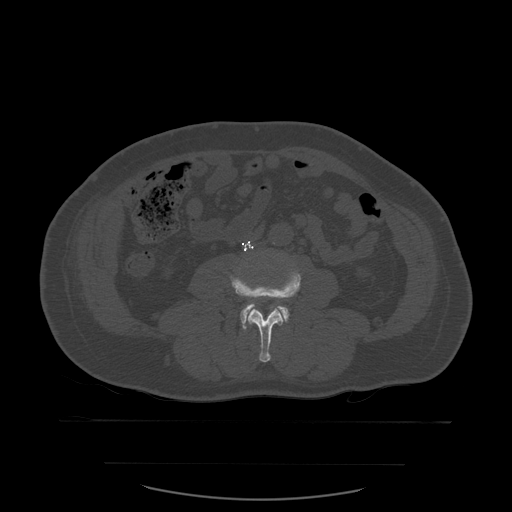
CT including the spine, one axial slice; position 183 of 590 along the scan axis; bone window (W 1800 / L 400 HU); 1.25 mm slice thickness; 512 × 512 image matrix, field of view 479 × 479 mm. Patient age 71 years. Case-level facts recorded for this patient, not image findings: primary cancer: lung.
Annotated regions visible in this slice (semi-automatically segmented with operator editing):
- L3 vertebra: bounding box <230,260,302,363> (left, top, right, bottom; pixels)
- L4 vertebra: <240,304,290,329>